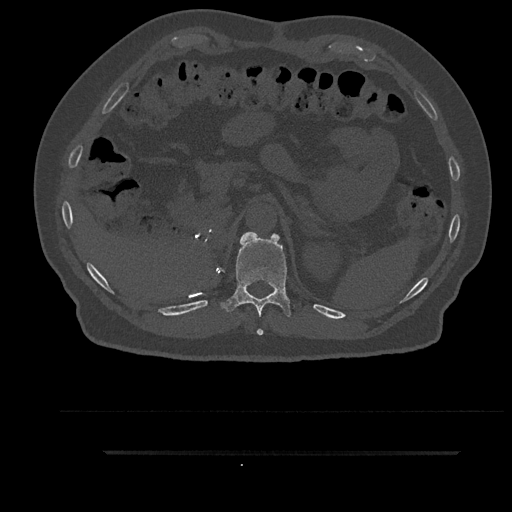
CT including the spine, one axial slice; bone window (W 1800 / L 400 HU); 0.5 mm slice thickness; 512 × 512 image matrix. Patient: male, 63 years. Case-level facts recorded for this patient, not image findings: primary cancer: renal; vertebrae with lytic lesions (as recorded): T8.
Outlined on this slice (semi-automatic segmentation, software-assisted and operator-edited):
- T11 vertebra: bounding box (x1, y1, x2, y2) in pixels: (220, 232, 296, 335)